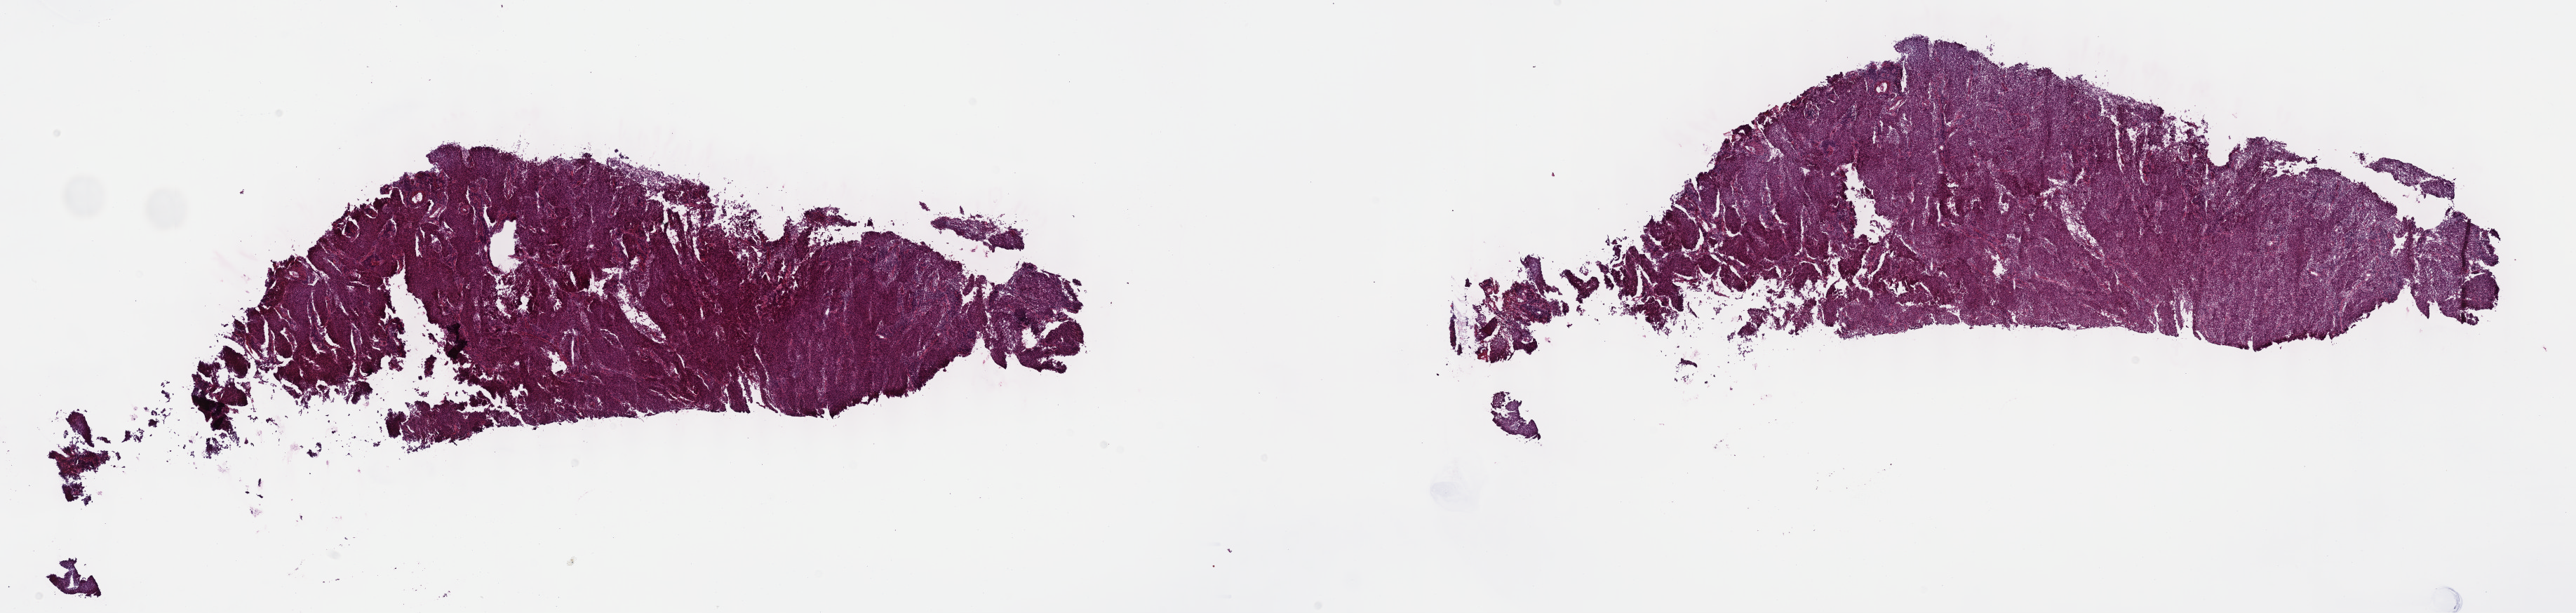
Hematoxylin and eosin (H&E) stained whole-slide image, low-resolution overview of the scanned area, about 29.7 x 7.1 mm (from a 40x scan); frozen section; primary tumour sample from the cervix. Female patient; age at initial diagnosis 46 years. Histologic grade: G2 (moderately differentiated). Slide review estimates, as recorded: tumour cells 85%, tumour nuclei 90%, normal cells 0%, stromal cells 15%, necrosis 0%. Infiltration values recorded for this section: lymphocyte infiltration 0%, monocyte infiltration 0%, neutrophil infiltration 0%.
Pathologic diagnosis: Squamous cell carcinoma, large cell, nonkeratinizing, NOS. FIGO stage: IIB.